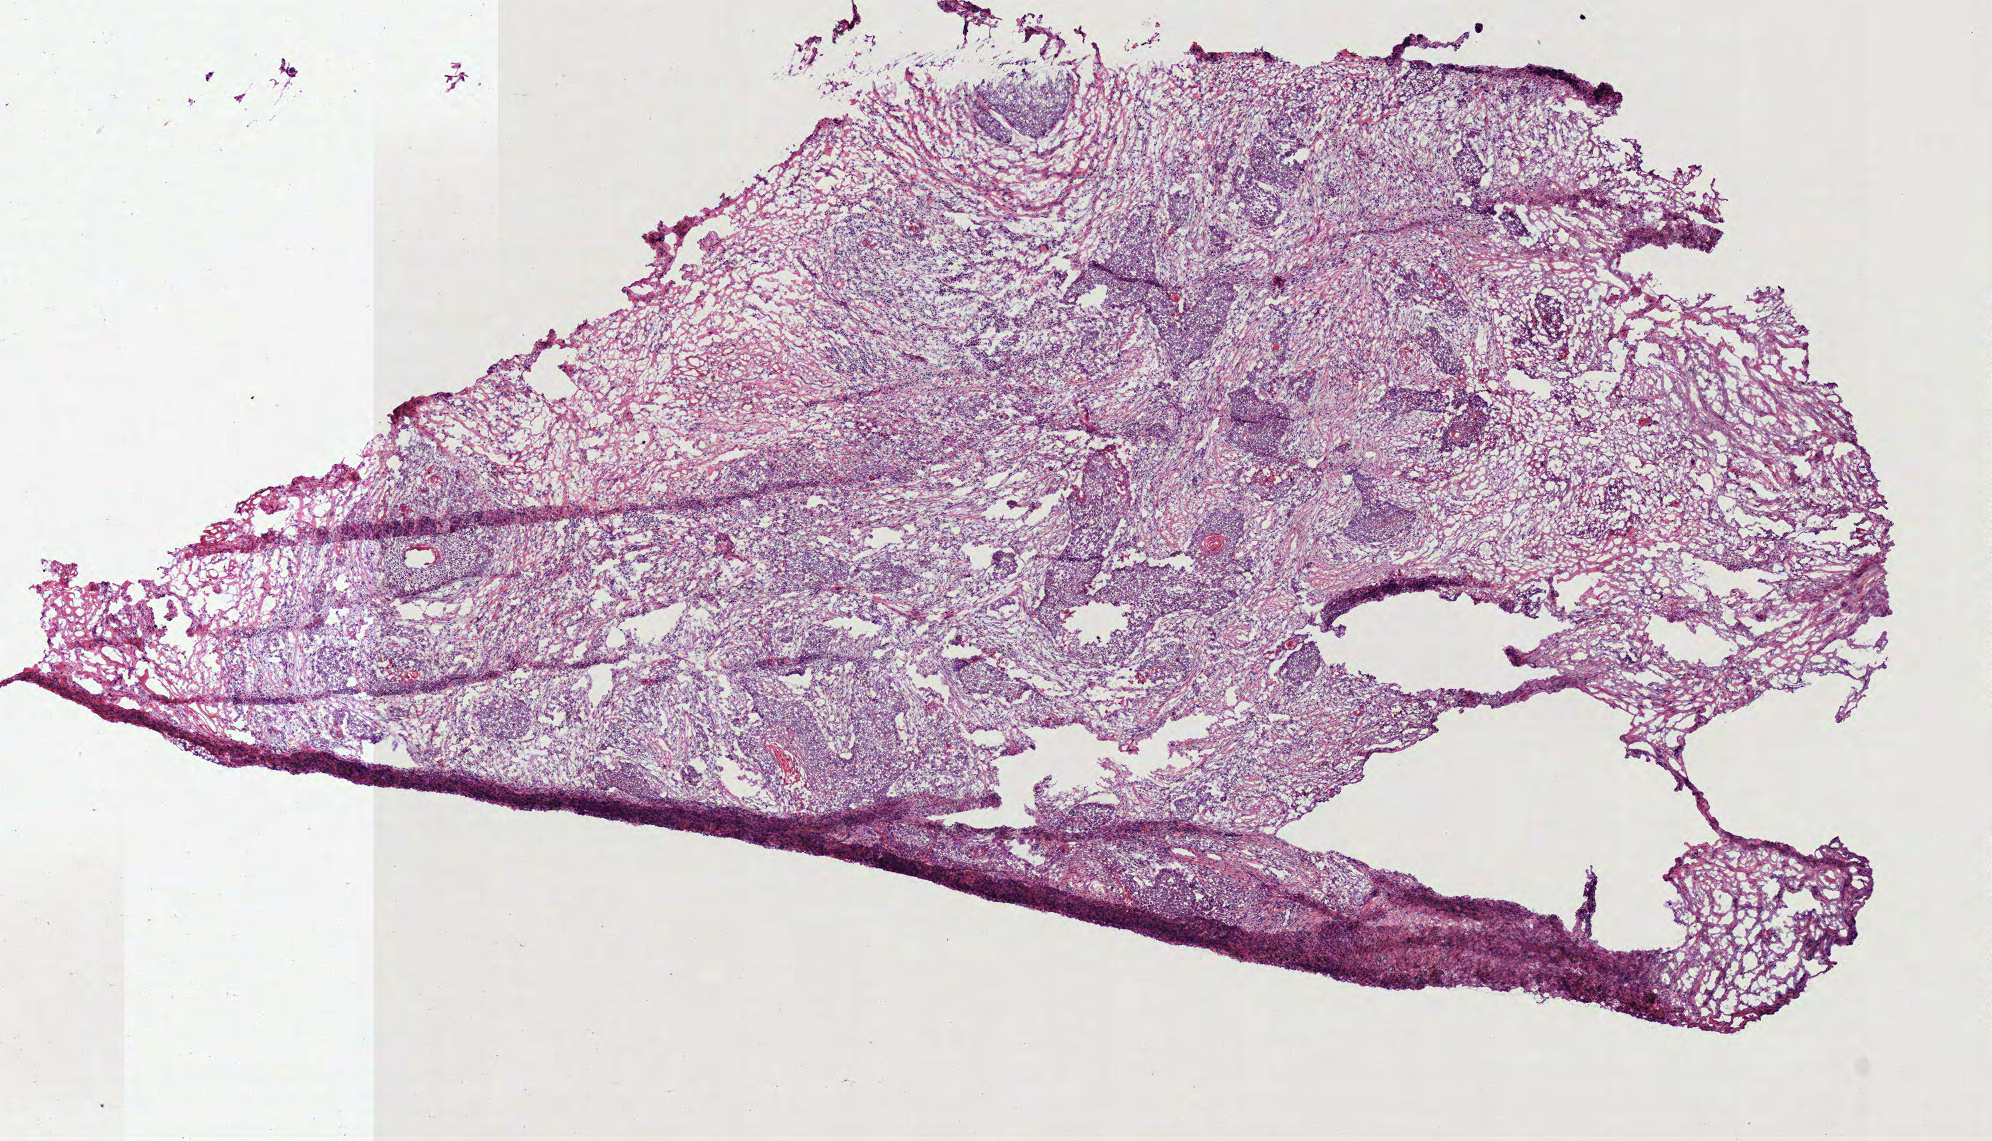
Digitized H&E tissue section (whole slide), low-resolution overview of the scanned area, about 7.8 x 4.5 mm (slide scanned at 40x). Frozen section from the top of the tissue portion. Primary tumour sample from the head and neck. Male, age 64 years at initial diagnosis. Histologic grade: G2 (moderately differentiated). Composition of this section per pathologist review: tumour cells 60%, tumour nuclei 65%, normal cells 0%, stromal cells 40%, necrosis 0%.
- AJCC pathologic stage: IVA (7th edition)
- pathologic diagnosis: Squamous cell carcinoma, NOS (larynx, NOS)